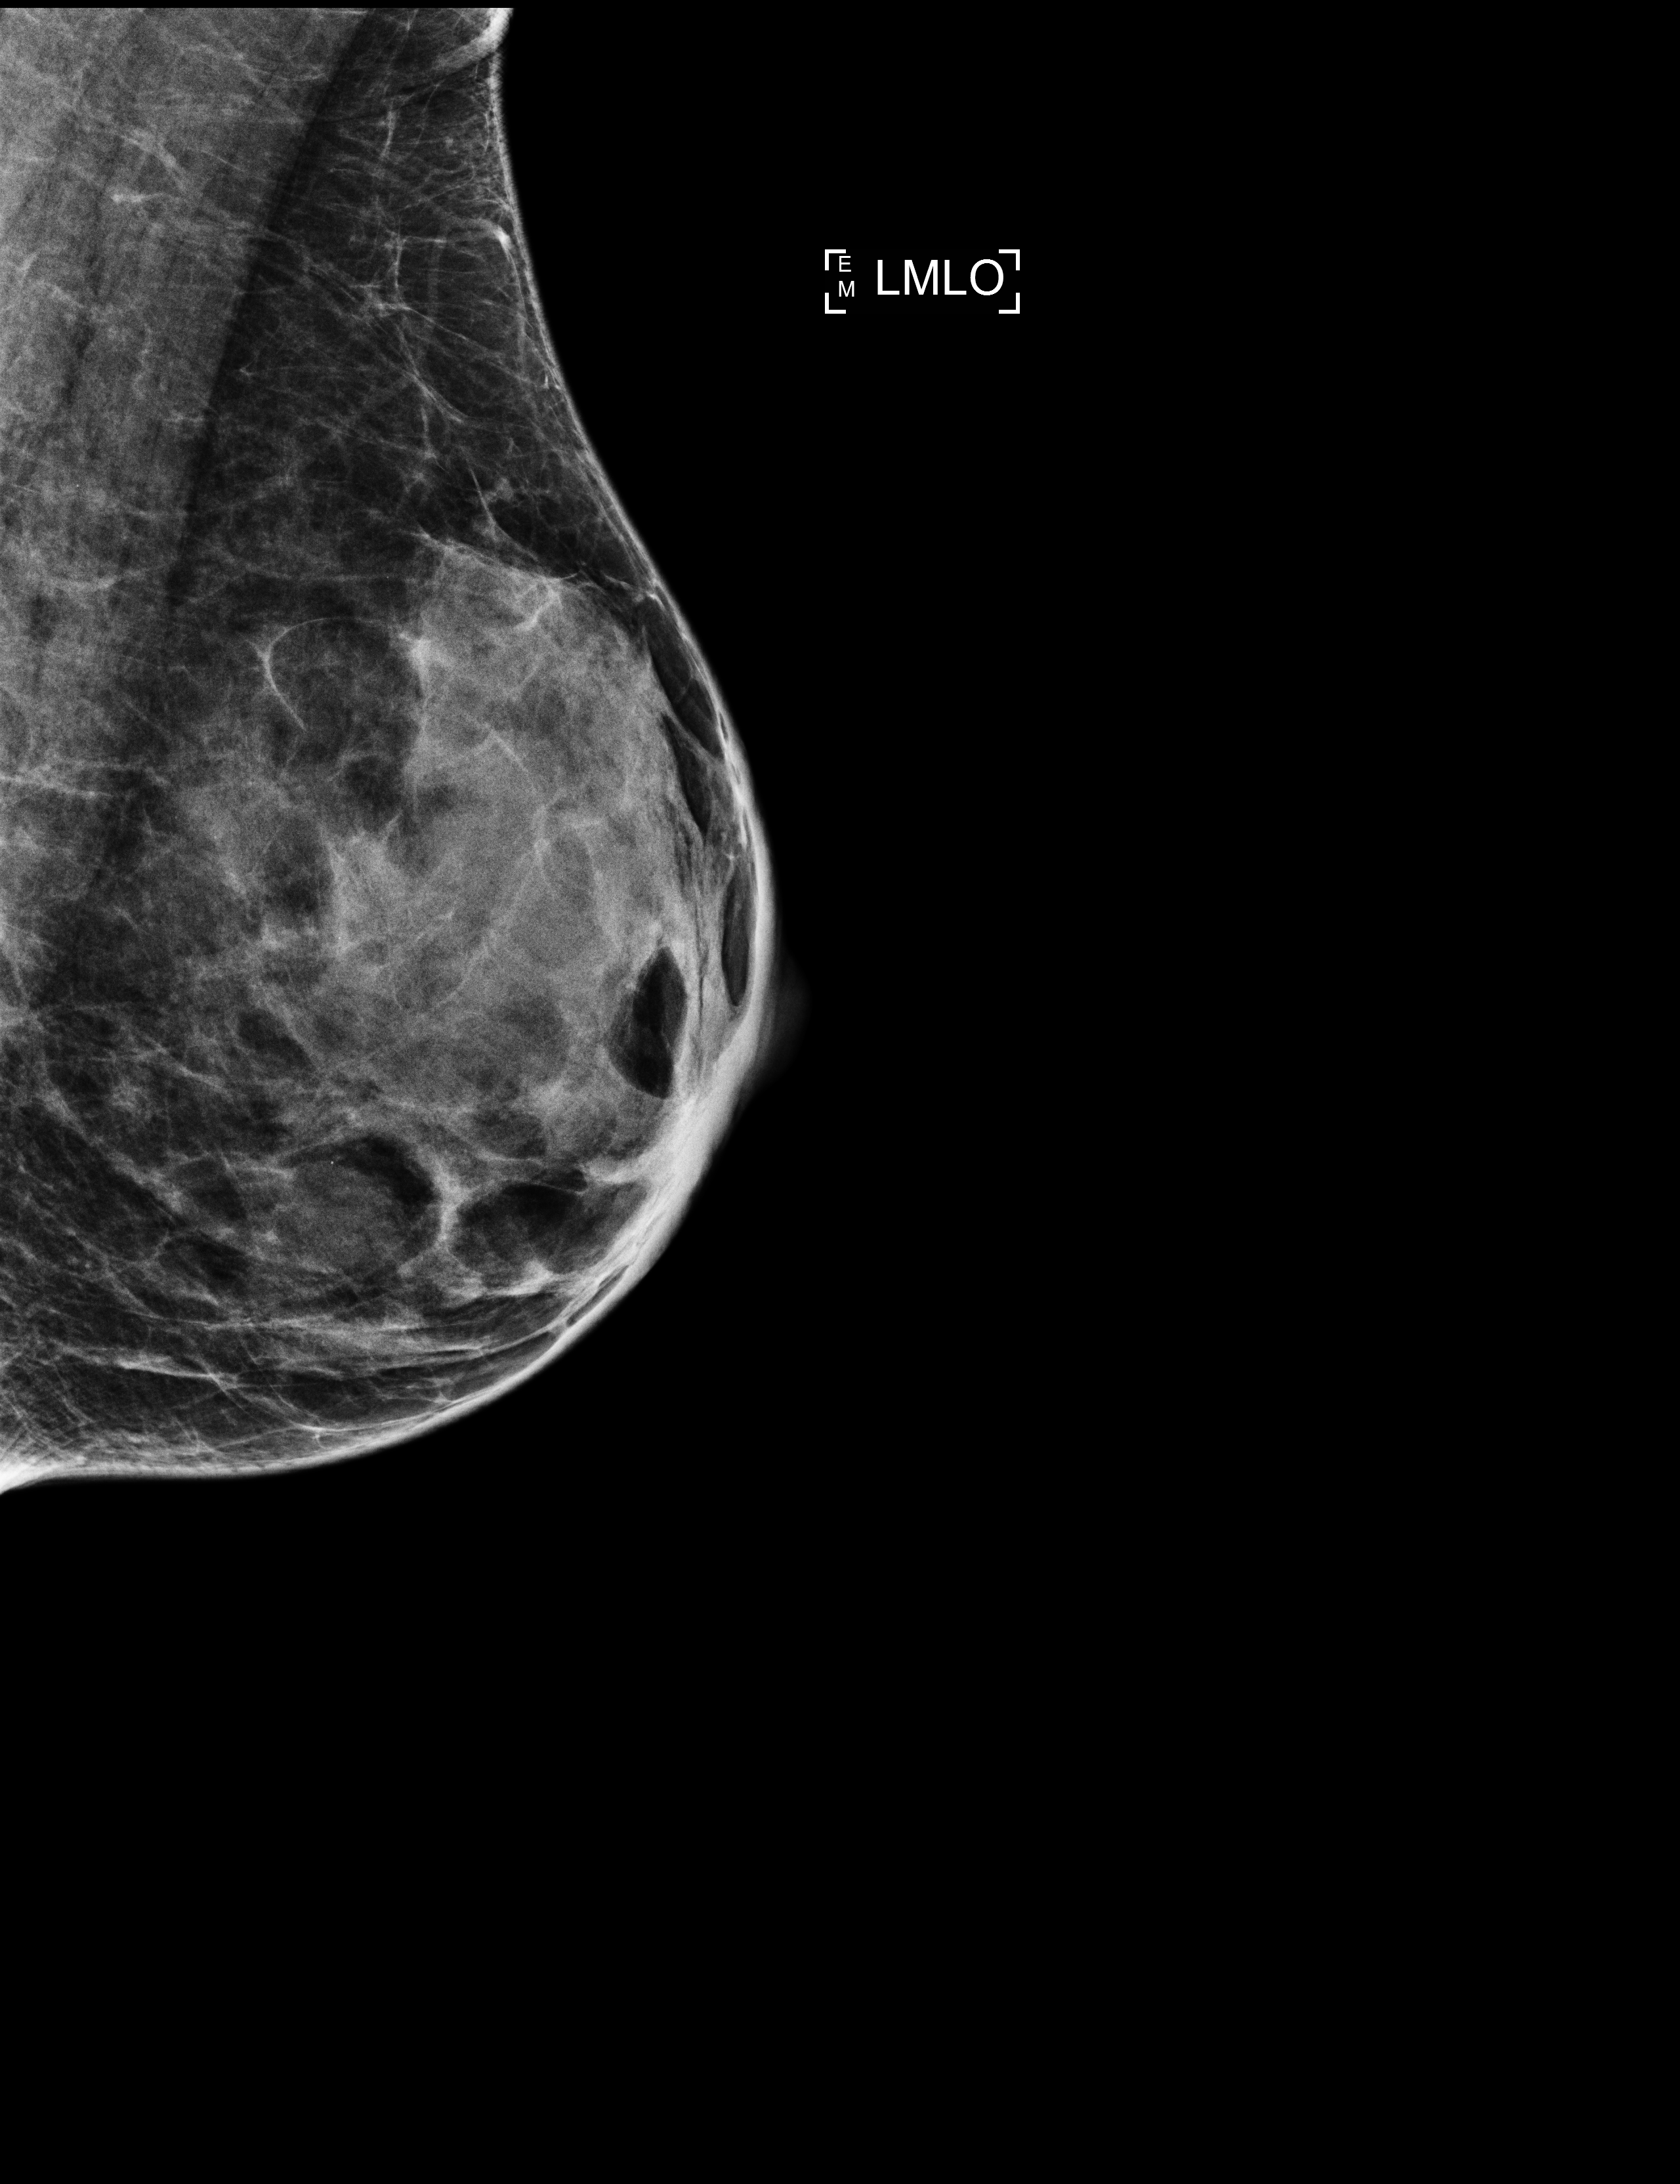
Screening examination, system: Selenia Dimensions. Female patient, age 66 years.
Image type: full-field digital mammogram. Breast: left. Projection: medio-lateral oblique projection.